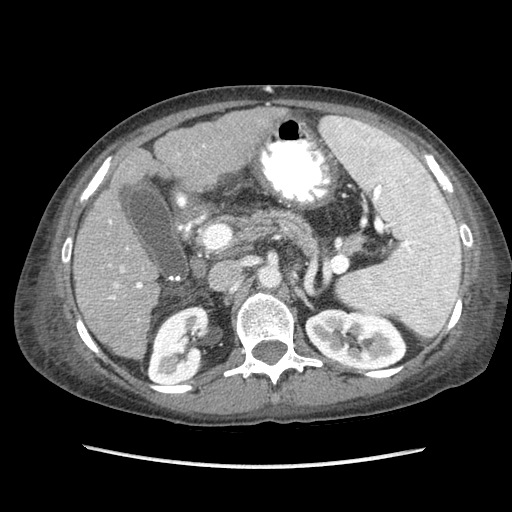
Contrast-enhanced abdominal CT (liver protocol), one axial slice. Position 40 of 87 along the scan axis. Reconstruction kernel STANDARD. 120 kVp. Soft-tissue window (W 400 / L 40 HU). 2.5 mm slice thickness. 512 × 512 image matrix, field of view 340 × 340 mm. Case-level facts recorded for this patient, not image findings: diagnosis: hepatocellular carcinoma (patient treated with transarterial chemoembolisation; whether this scan precedes or follows treatment is not stated here); TNM stage (as recorded): Stage-IIIB; Child-Pugh class: A; tumour differentiation: no biopsy; tumour nodularity: uninodular.
Structures marked on this image (semi-automatically segmented with operator editing):
- liver parenchyma outside the tumour (the mass and vessels are separate outlines, so this box may not span the whole liver): bounding box [x1, y1, x2, y2] px = [74, 108, 284, 358]
- liver vessels: [108, 145, 205, 321]